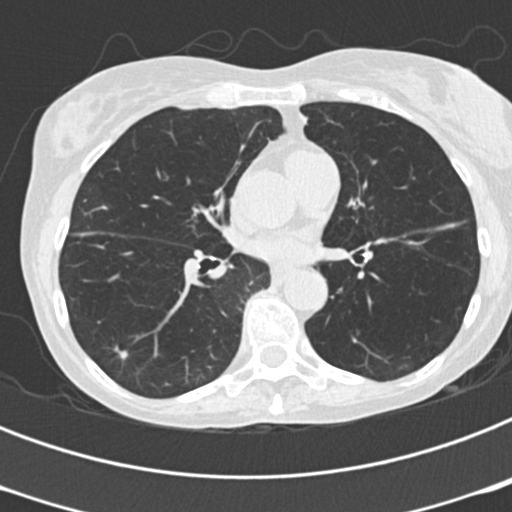
Low-dose screening chest CT, axial slice; third annual screen; lung window (W 1500 / L -600 HU); 2 mm slice thickness; standard (soft-tissue) reconstruction kernel (B30f); 512 × 512 image matrix, field of view 290 × 290 mm. Female participant, aged 68 years at enrolment. Former smoker at enrolment.
- Expert-annotated lung lesion, bounding box [x1, y1, x2, y2] px = [102, 337, 140, 368].
- The exam's reader record, not a measurement of the box and not confirmed to be the same lesion: non-calcified nodule or mass ≥4 mm, right lower lobe, 9 × 5 mm, poorly defined margins, soft tissue attenuation, pre-existing on the prior screen: yes; interval growth: no.